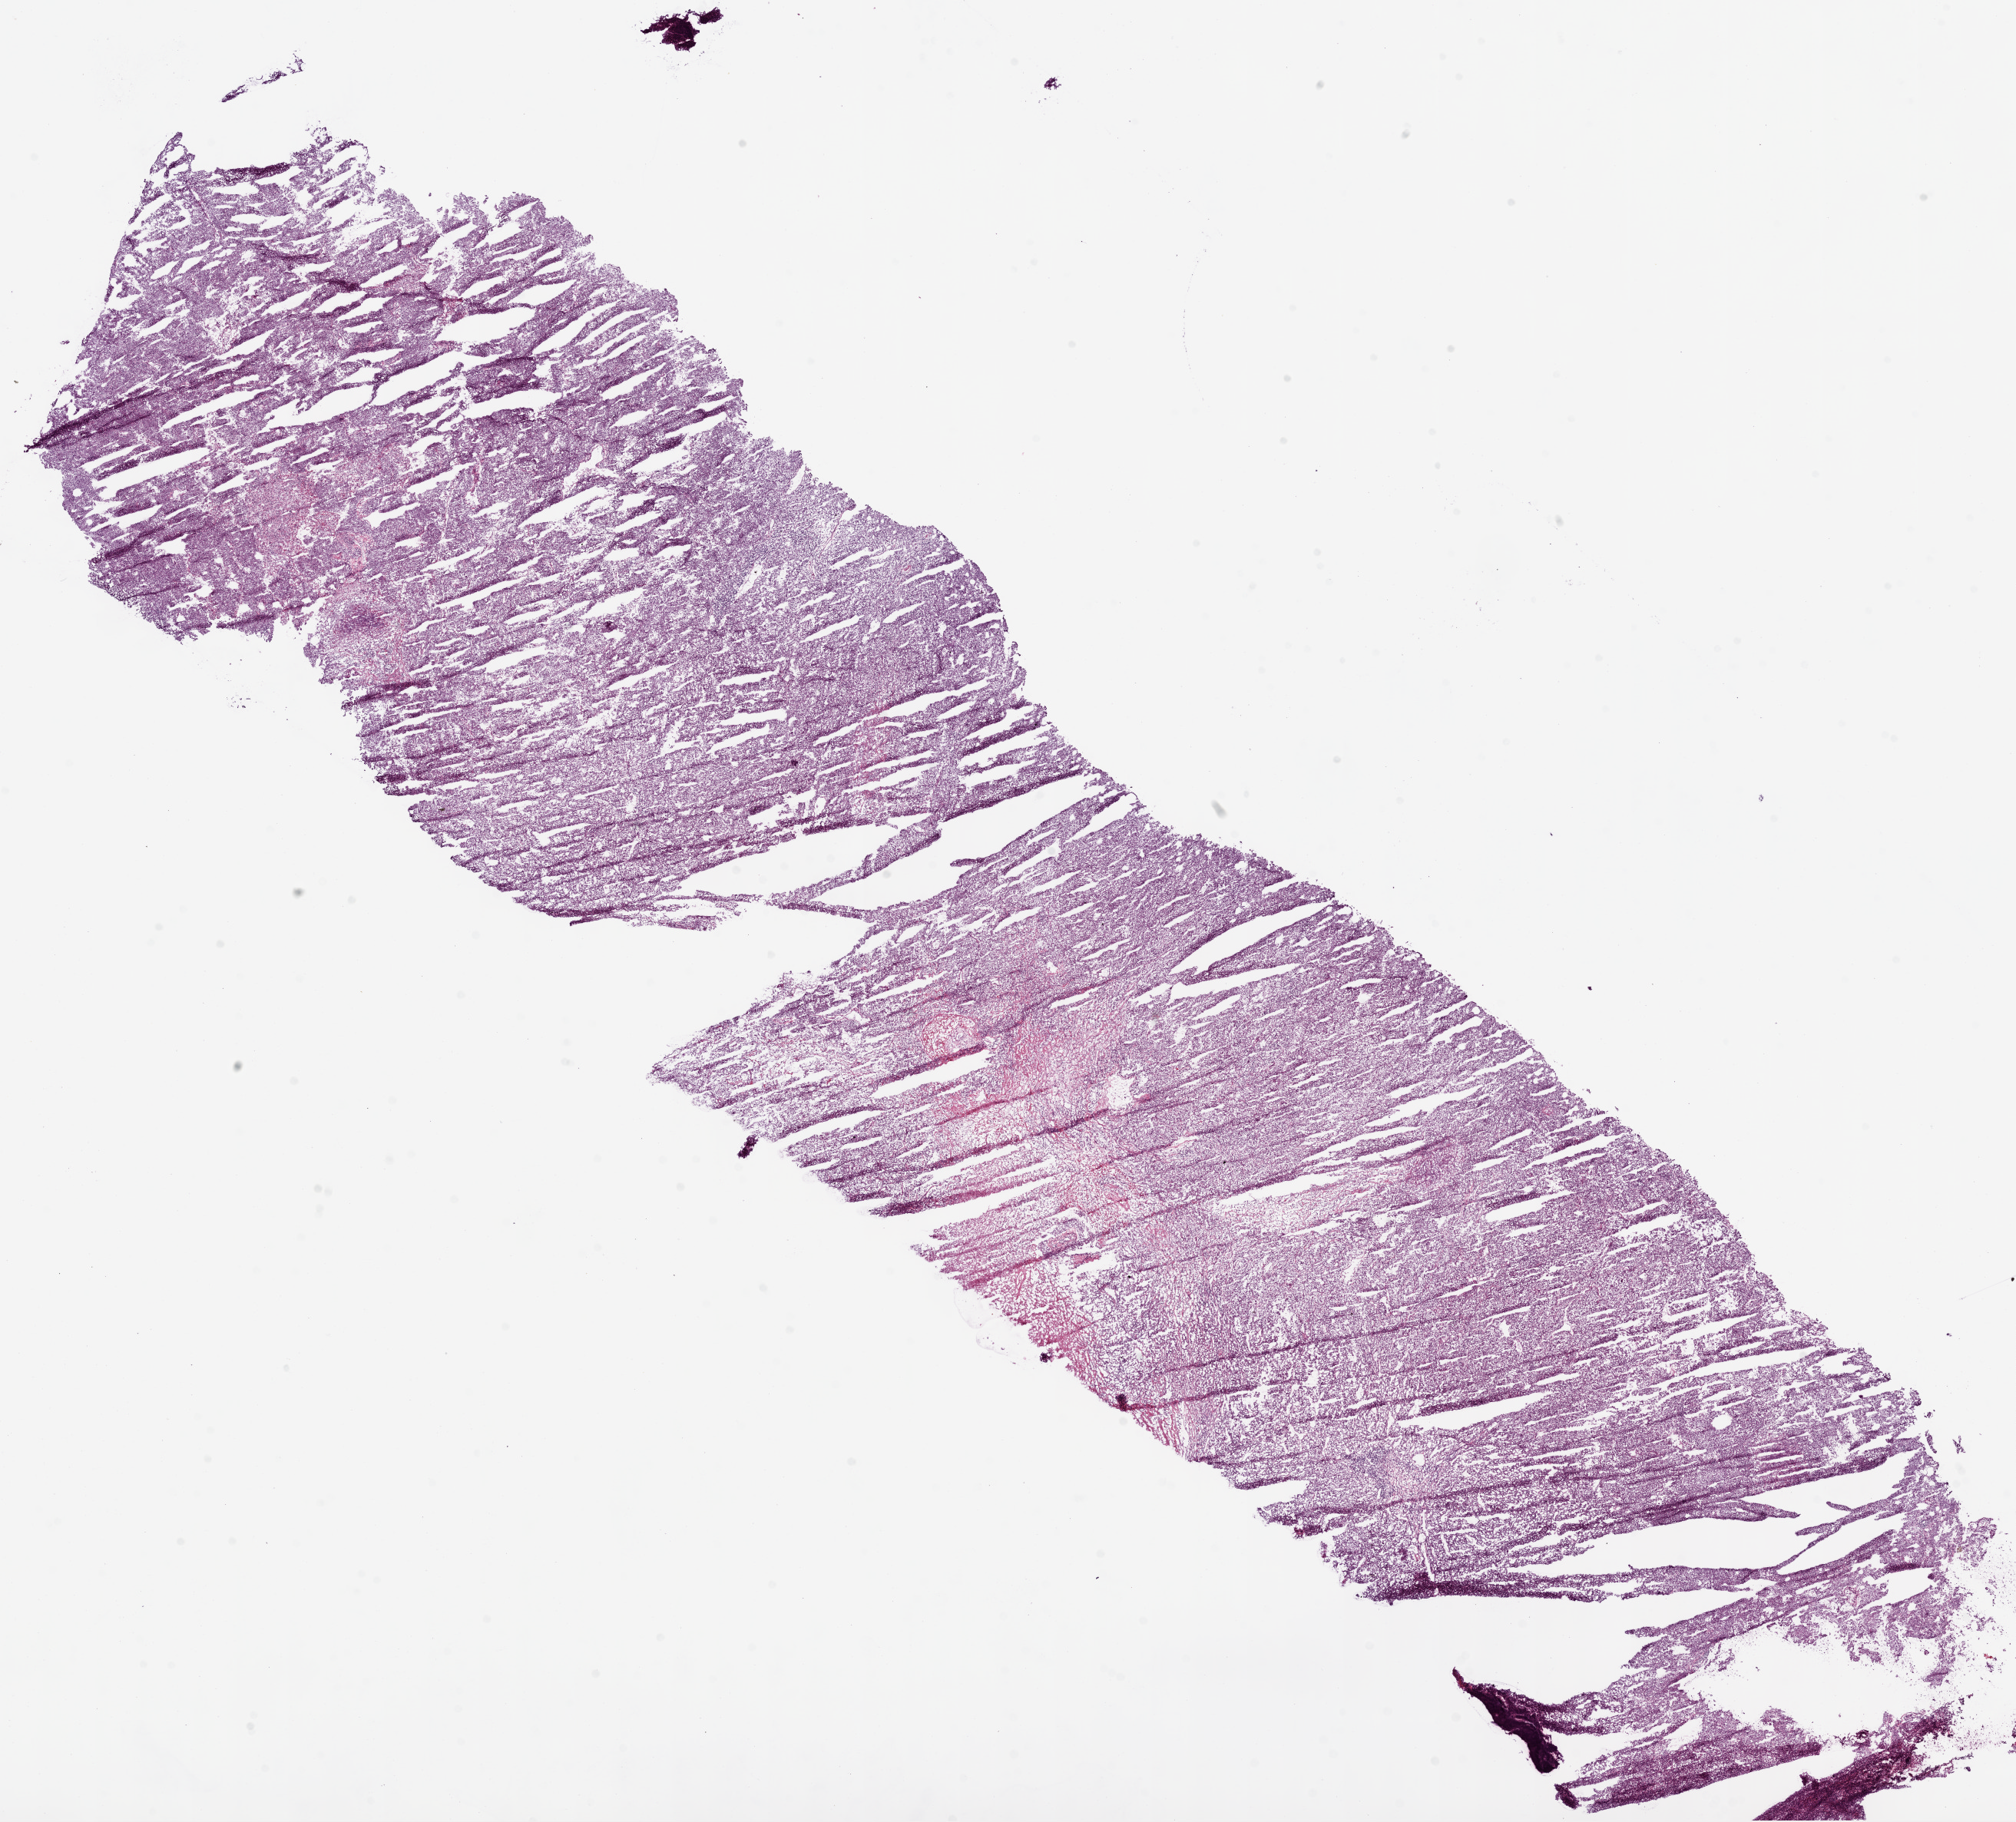
Whole-slide histology image, Hematoxylin and eosin (H&E) stained, shown as a low-resolution overview of the whole scanned area (about 21.1 x 19.0 mm, slide scanned at 20x); frozen section from the top of the tissue portion; kidney, primary tumour sample. Patient: male, age at initial diagnosis 81 years. Histologic grade: G3 (poorly differentiated). Composition of this section per pathologist review: tumour cells 90%, tumour nuclei 85%, normal cells 0%, stromal cells 5%, necrosis 5%.
AJCC pathologic stage: III. Histologic diagnosis: Clear cell adenocarcinoma, NOS. Laterality: right.